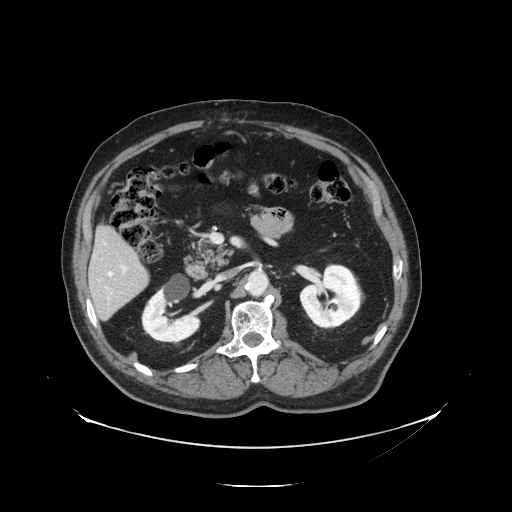
Contrast-enhanced abdominal CT, one axial slice. Position 61 of 138 along the scan axis. Intravenous contrast given. Soft-tissue window (W 400 / L 40 HU). 2.5 mm slice thickness. 512 × 512 image matrix, field of view 497 × 497 mm. Male patient, age 77 years. From the clinical record (not read from this slice): diagnosis: colorectal cancer liver metastases, imaged before liver resection; multiple liver metastases: no; largest metastasis: 1.5 cm; disease in both lobes: no.
Outlined on this slice (expert manual segmentation):
- liver: box from (x=91, y=227) to (x=148, y=320) px
- planned liver remnant (the part of the liver to remain after resection): (x=91, y=227)–(x=143, y=285)
- portal vein (with intrahepatic branches): (x=123, y=267)–(x=126, y=269)